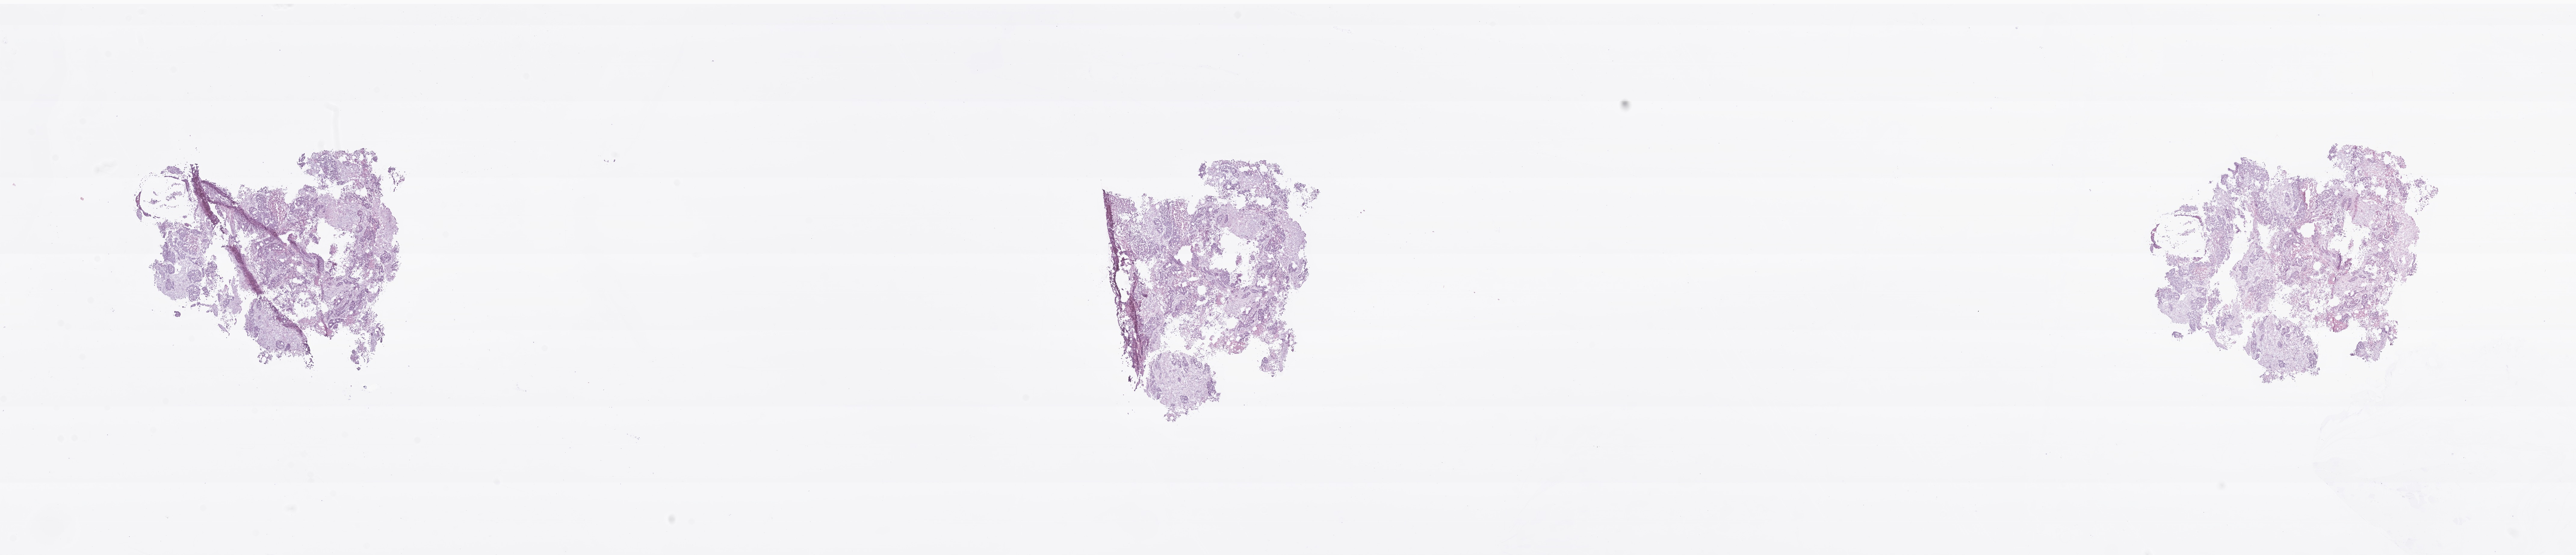
Digitized H&E-stained section of tumor tissue from the intestinal tract, shown as a low-resolution overview of the whole scanned area (about 36.0 x 7.7 mm); frozen section. Patient: female, age 277 months (23 years 1 month).
Diagnosis (ICD-O-3 morphology term): Carcinoma, metastatic, NOS.